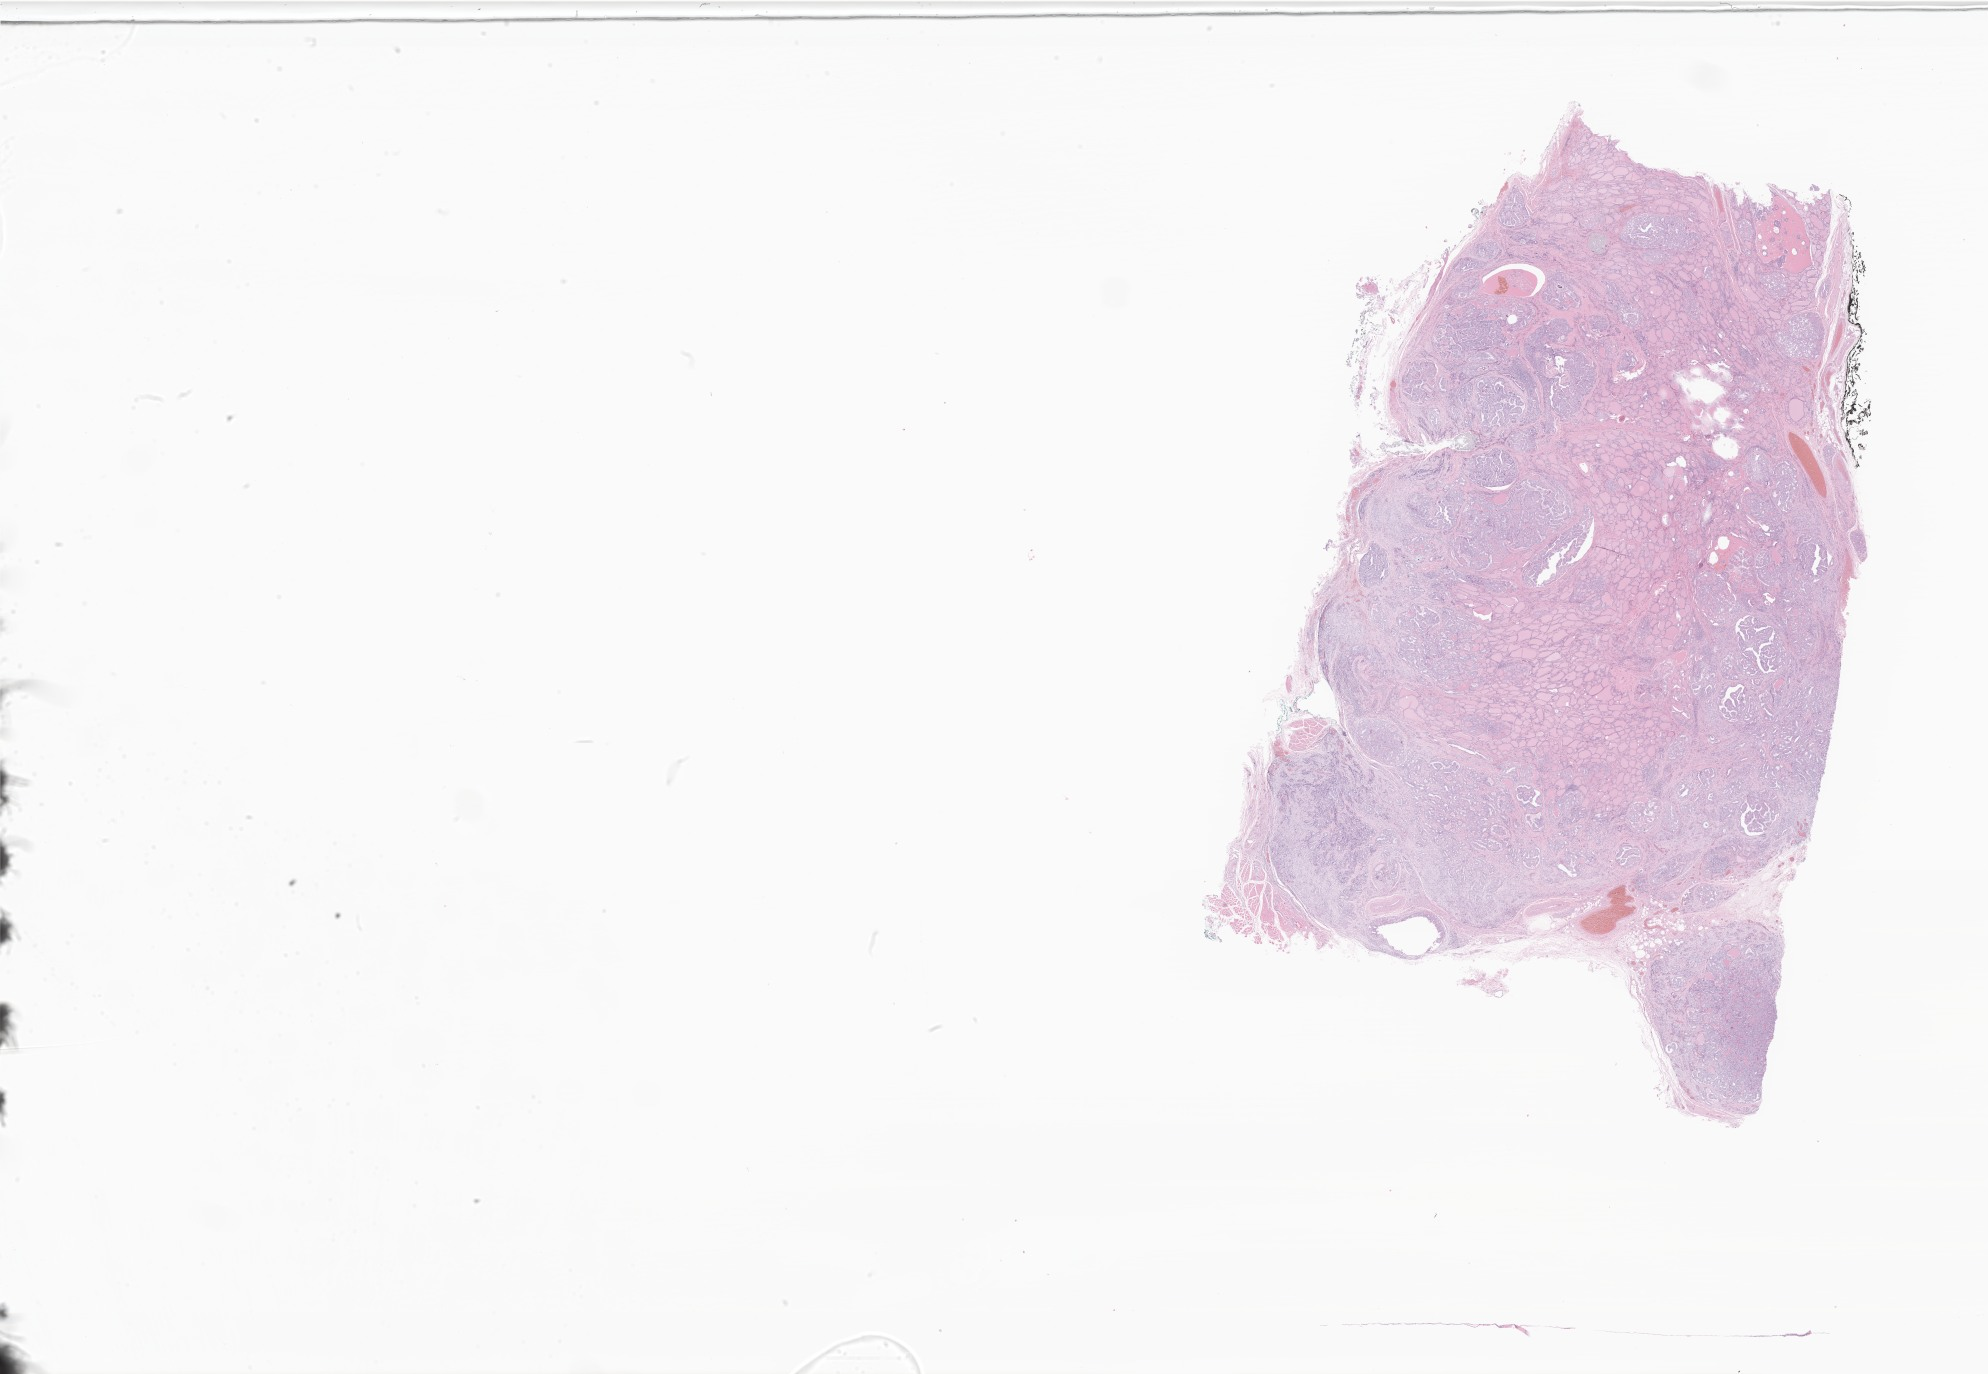
Digitized hematoxylin and eosin (H&E)-stained section of tumor tissue from the lymph node — shown as a low-resolution overview of the whole scanned area (about 33.5 x 23.2 mm), formalin-fixed, paraffin-embedded (FFPE) tissue. Patient female; age 88 months (7 years 4 months).
- diagnosis: Papillary carcinoma, NOS